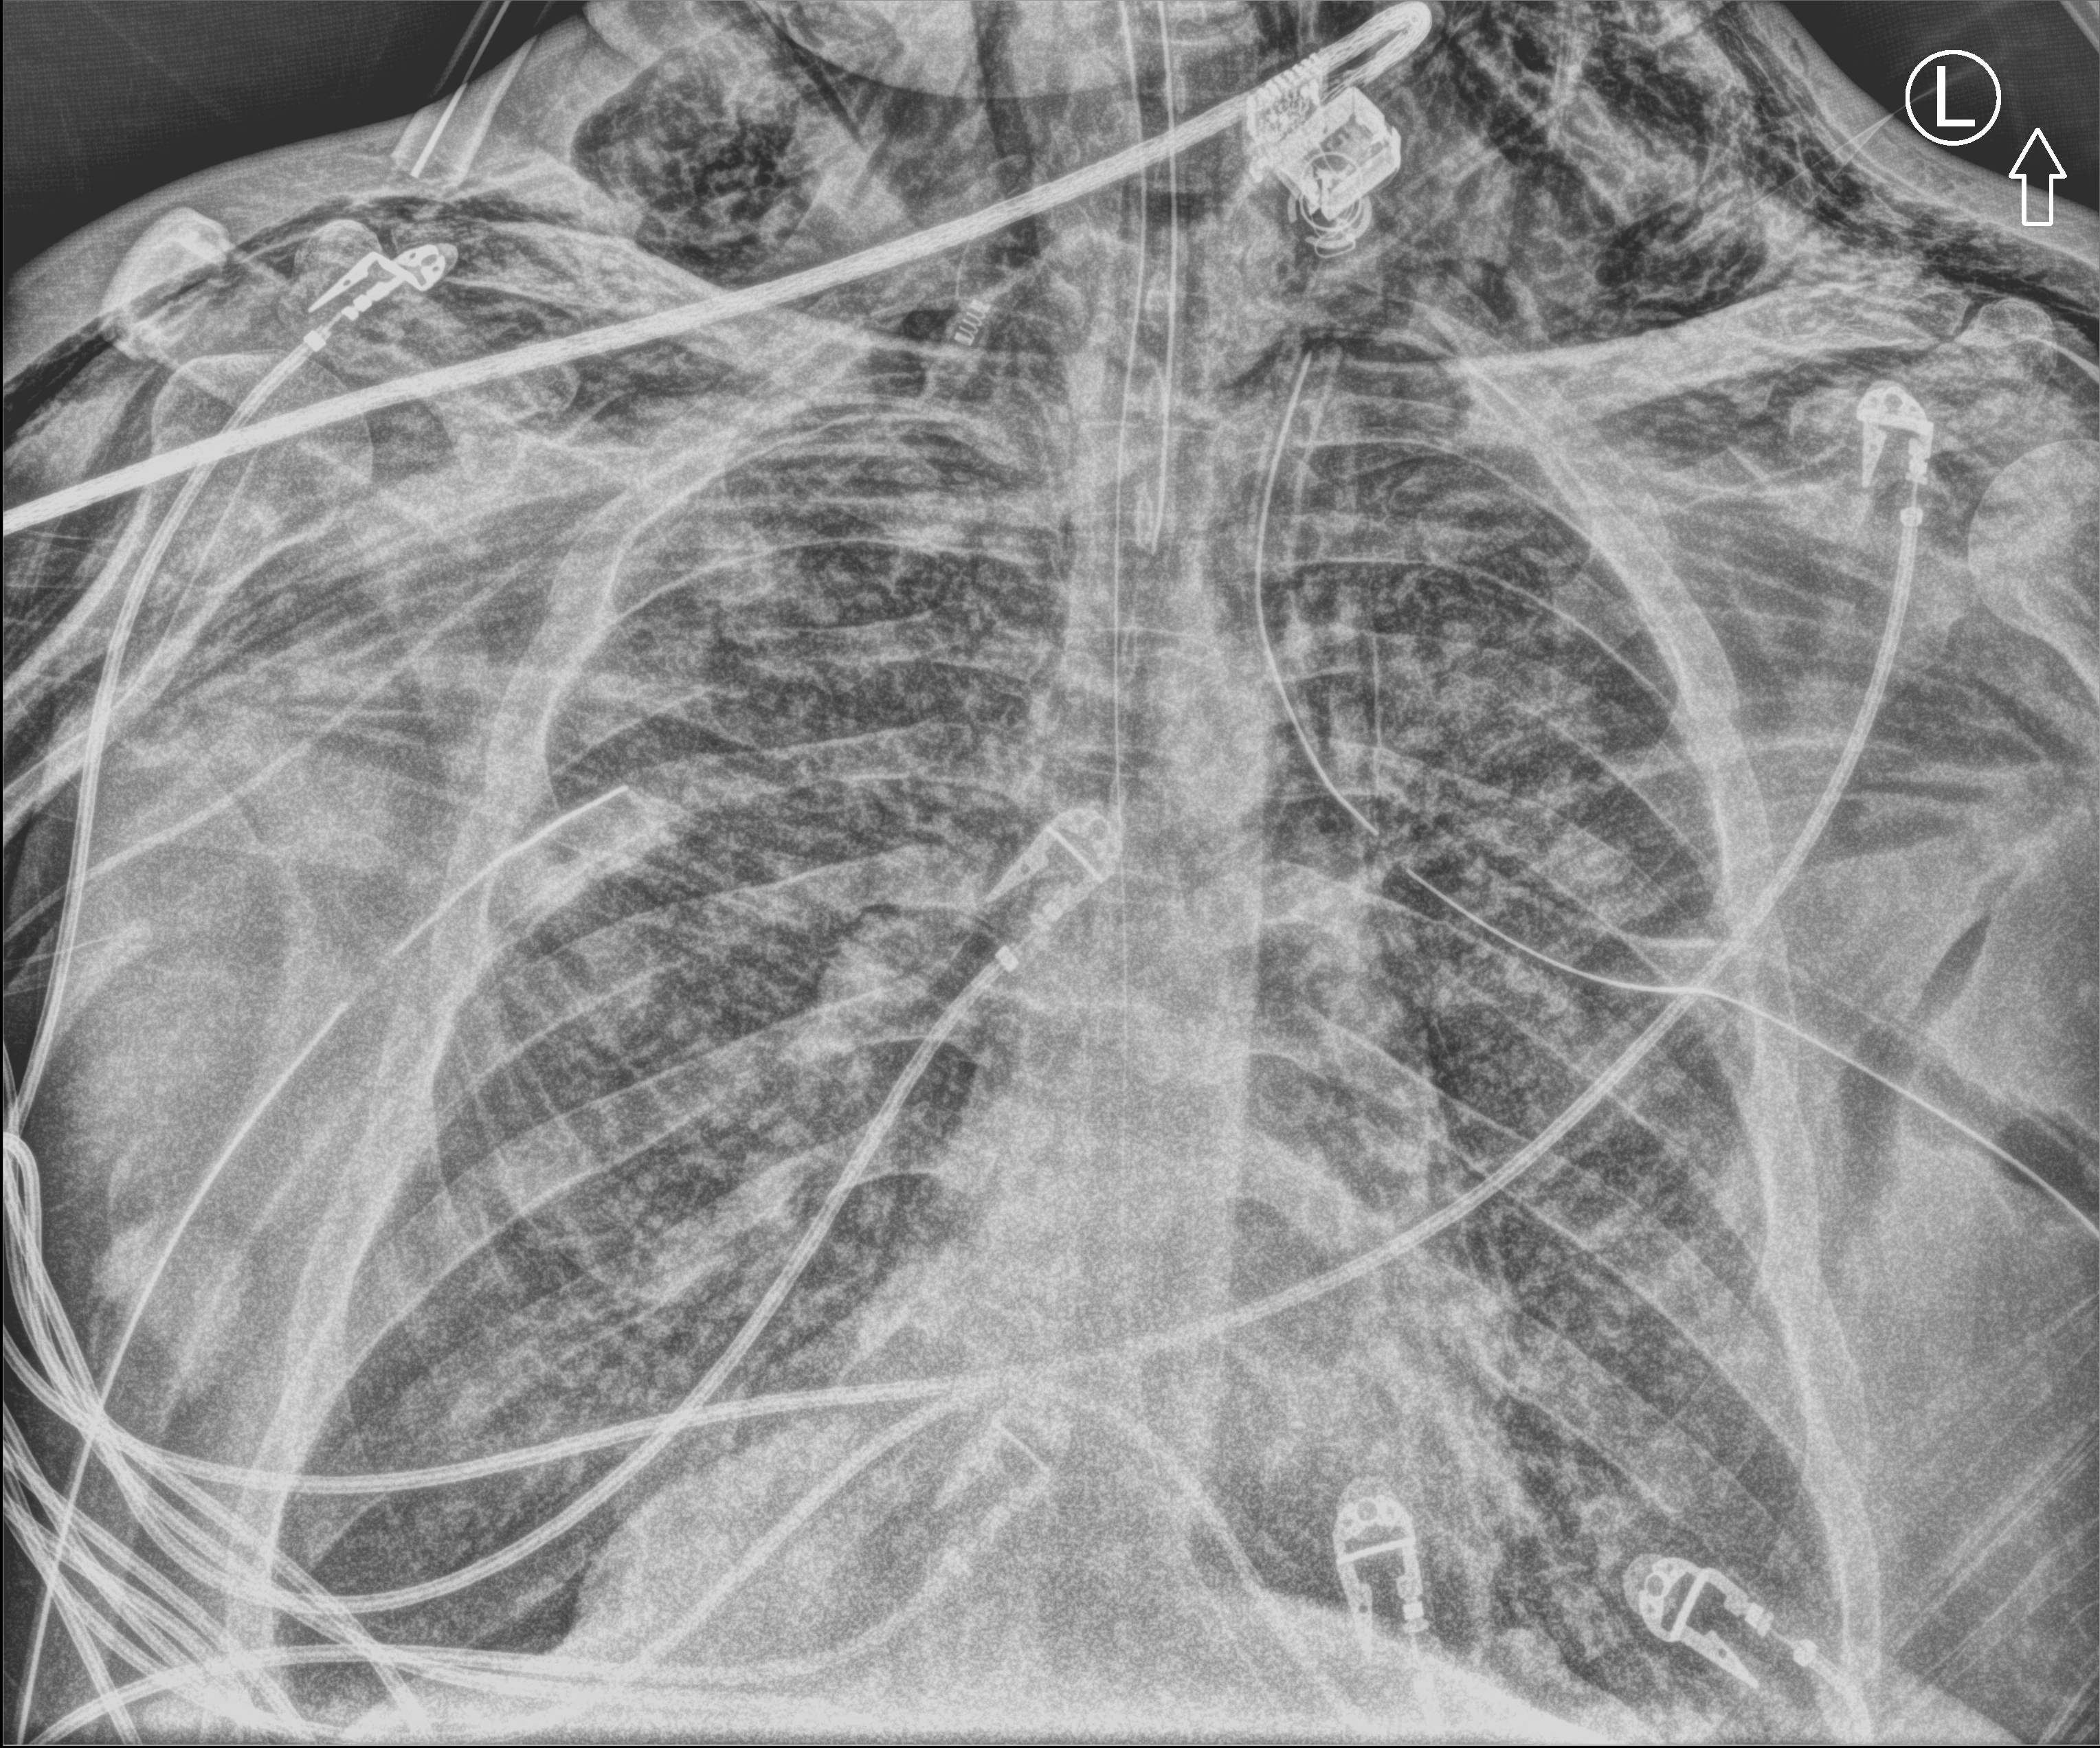
Portable chest radiograph; anteroposterior (AP) projection. Patient hospitalised with COVID-19, aged 18–59 years.
Hospital-stay facts (about this admission, not read from this image; timing relative to this image not recorded): length of hospital stay: 15 days; mechanically ventilated during this hospital stay: yes; admitted to intensive care during this hospital stay: yes.